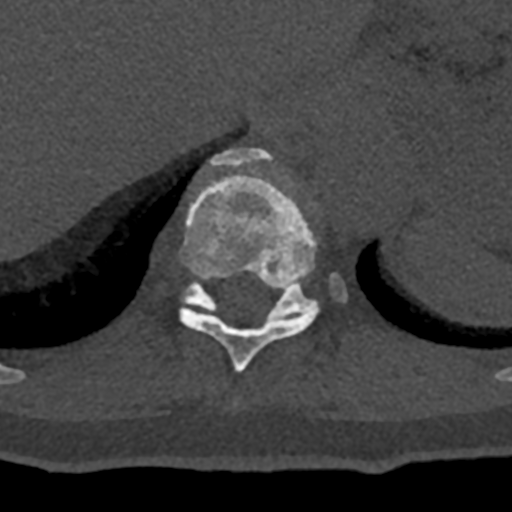
CT including the spine, one axial slice; position 587 of 797 along the scan axis; reconstruction kernel Br40s/3; 120 kVp; bone window (W 1800 / L 400 HU); 512 × 512 image matrix. Male patient, age 74 years. Case-level facts recorded for this patient, not image findings: primary cancer: renal; vertebrae with lytic lesions (as recorded): T10, L1, L2, L3, L4, L5.
Structures marked on this image (semi-automatic segmentation, software-assisted and operator-edited):
- T10 vertebra: box from (x=180, y=148) to (x=319, y=372) px
- T11 vertebra: (x=182, y=273)–(x=346, y=319)